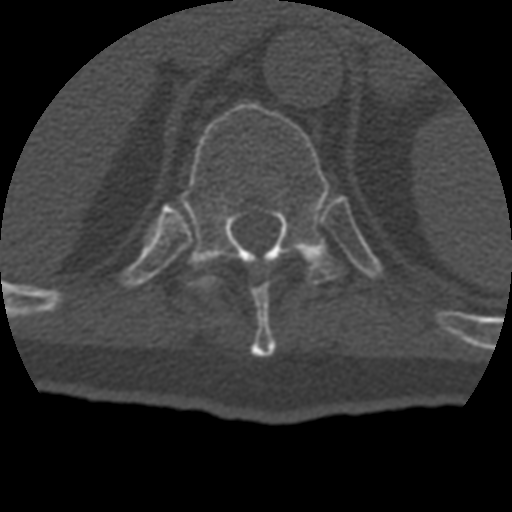
CT including the spine, one axial slice. Slice 204 of 399 in the series (ordered by position). Reconstruction kernel STANDARD. 120 kVp. Bone window (W 1800 / L 400 HU). 1.25 mm slice thickness. 512 × 512 image matrix, field of view 160 × 160 mm. Patient age 69 years. Case-level facts recorded for this patient, not image findings: primary cancer: prostate.
Annotated regions visible in this slice (semi-automatic segmentation, software-assisted and operator-edited):
- T10 vertebra: bounding box [x1, y1, x2, y2] px = [251, 286, 276, 357]
- T11 vertebra: [180, 102, 347, 290]